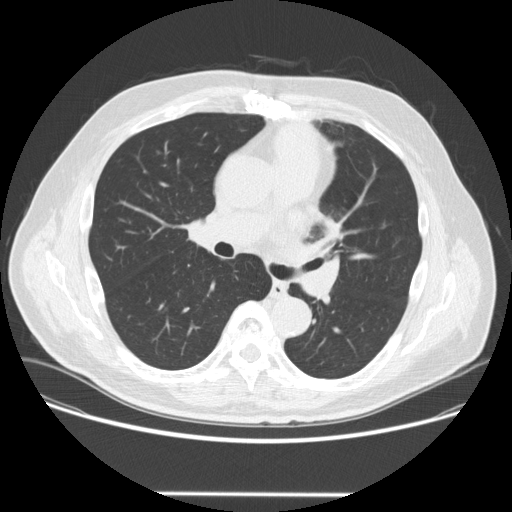
Axial slice from a low-dose chest CT screening exam, third annual screen, lung window (W 1500 / L -600 HU), 2.5 mm slice thickness, standard (soft-tissue) reconstruction kernel (STANDARD), 120 kVp, slice 100 of 253 in the series. Male participant, aged 66 years at enrolment.
Expert-annotated lung lesion, box from (x=300, y=209) to (x=352, y=256) px. The screening reader recorded 2 non-calcified nodules or masses ≥4 mm on this exam (left upper lobe, right lower lobe); which of them this box marks is not recorded.